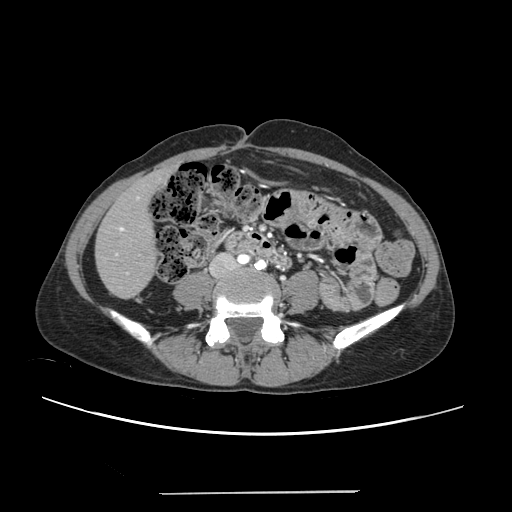
Contrast-enhanced abdominal CT, one axial slice; slice 46 of 240 in the series (ordered by position); 120 kVp; intravenous contrast given; soft-tissue window (W 400 / L 40 HU); 1.25 mm slice thickness; 512 × 512 image matrix, field of view 371 × 371 mm. Female patient, age 60 years. Case-level facts recorded for this patient, not image findings: diagnosis: colorectal cancer liver metastases, imaged before liver resection; multiple liver metastases: no; largest metastasis: 1.5 cm.
Structures marked on this image (manually delineated by an expert):
- liver: box from (x=96, y=170) to (x=169, y=297) px
- planned liver remnant (the part of the liver to remain after resection): (x=96, y=171)–(x=167, y=297)
- portal vein (with intrahepatic branches): (x=115, y=196)–(x=139, y=274)